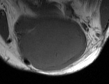
MRI of an extremity soft-tissue mass, one axial slice; position 22 of 50 along the scan axis; MR volume resampled by the dataset authors to the PET/CT grid (not the native acquisition matrix); 109 × 84 image matrix, field of view 106 × 82 mm. Male patient. Case-level facts recorded for this patient, not image findings: histological type: synovial sarcoma; site of the primary tumour: left poplietal fossa.
Annotated regions visible in this slice (expert contour drawn on MRI and transferred to this co-registered scan by the dataset authors):
- gross tumour volume (mass): bounding box <16,21,88,72> (left, top, right, bottom; pixels)